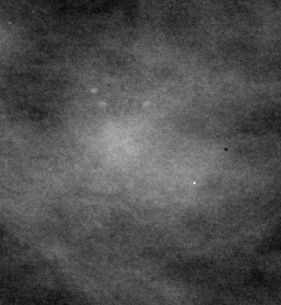
Cropped region of a digitized screen-film mammogram centred on a radiologist-marked abnormality; left breast; MLO view; BI-RADS breast density category 3 (scale 1–4).
- Calcifications, morphology pleomorphic, distribution clustered; BI-RADS assessment category 4; pathology result (as recorded, not read from the image): benign.